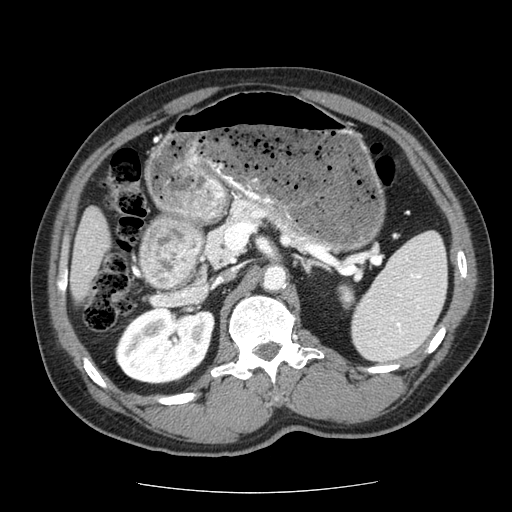
Contrast-enhanced abdominal CT (liver protocol), one axial slice. Slice 17 of 85 in the series (ordered by position). Soft-tissue window (W 400 / L 40 HU). 2.5 mm slice thickness. 512 × 512 image matrix. Case-level facts recorded for this patient, not image findings: diagnosis: hepatocellular carcinoma (patient treated with transarterial chemoembolisation; whether this scan precedes or follows treatment is not stated here); TNM stage (as recorded): Stage-IIIA; Child-Pugh class: A; tumour differentiation: well differentiated; tumour nodularity: multinodular.
Annotated regions visible in this slice (semi-automatic segmentation, software-assisted and operator-edited):
- liver parenchyma outside the tumour (the mass and vessels are separate outlines, so this box may not span the whole liver): bounding box [x1, y1, x2, y2] px = [70, 206, 110, 302]